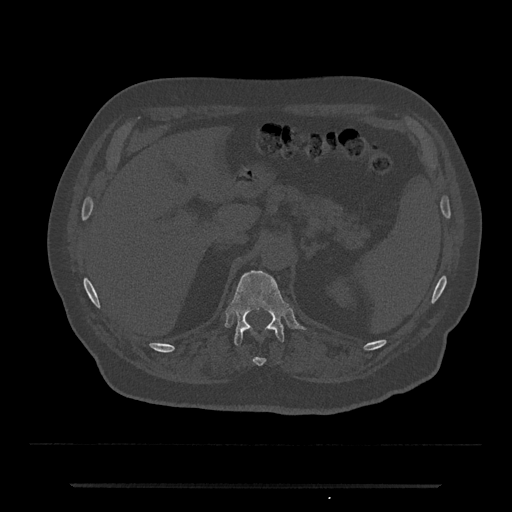
CT including the spine, one axial slice; position 607 of 797 along the scan axis; 120 kVp; bone window (W 1800 / L 400 HU); 0.5 mm slice thickness; 512 × 512 image matrix, field of view 434 × 434 mm. Male patient, age 80 years. From the clinical record (not read from this slice): primary cancer: prostate.
Structures marked on this image (semi-automatic segmentation, software-assisted and operator-edited):
- T11 vertebra: bounding box (x1, y1, x2, y2) in pixels: (253, 357, 265, 366)
- T12 vertebra: (228, 270, 289, 346)